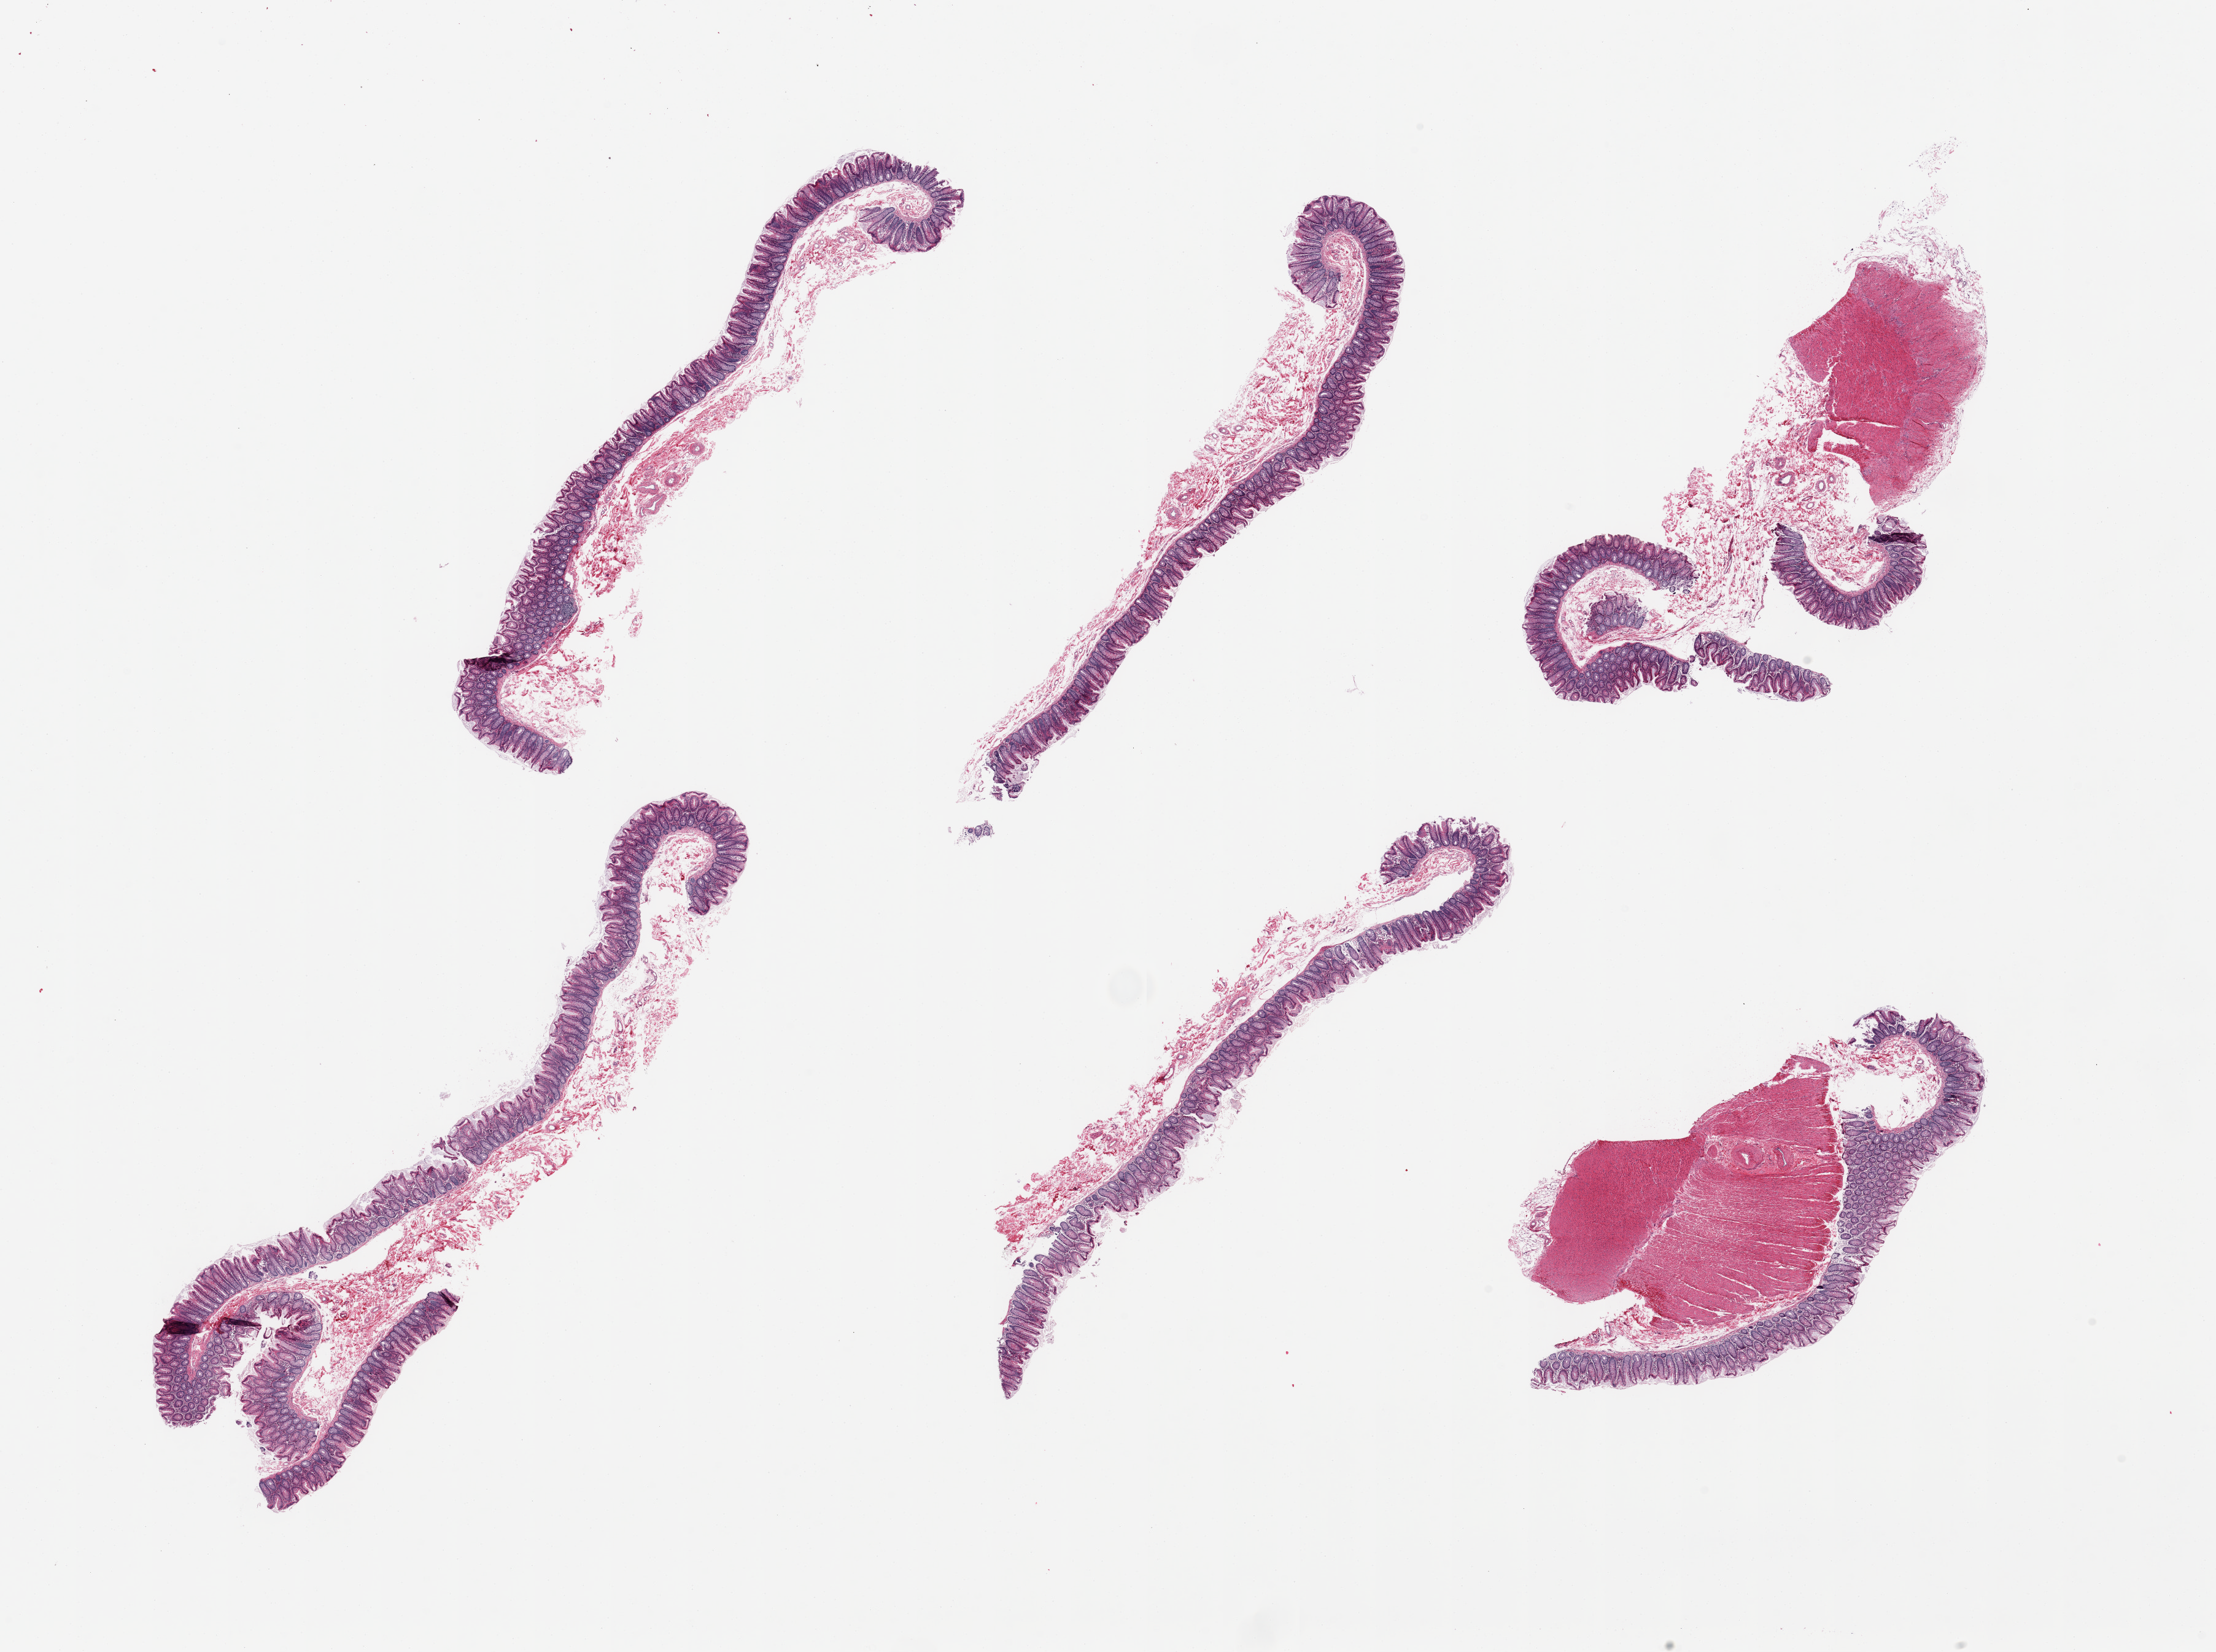
Whole-slide image, haematoxylin and eosin stain — shown as a low-resolution overview of the whole scanned area (about 28.5 x 21.3 mm), PAXgene-fixed, paraffin-embedded tissue, section of transverse colon (target tissue), tissue donor sample. Donor sex: male.
Pathologist's review note for this sample: 6 pieces, mucosa up to ~0.3mm, ~40% thickness.